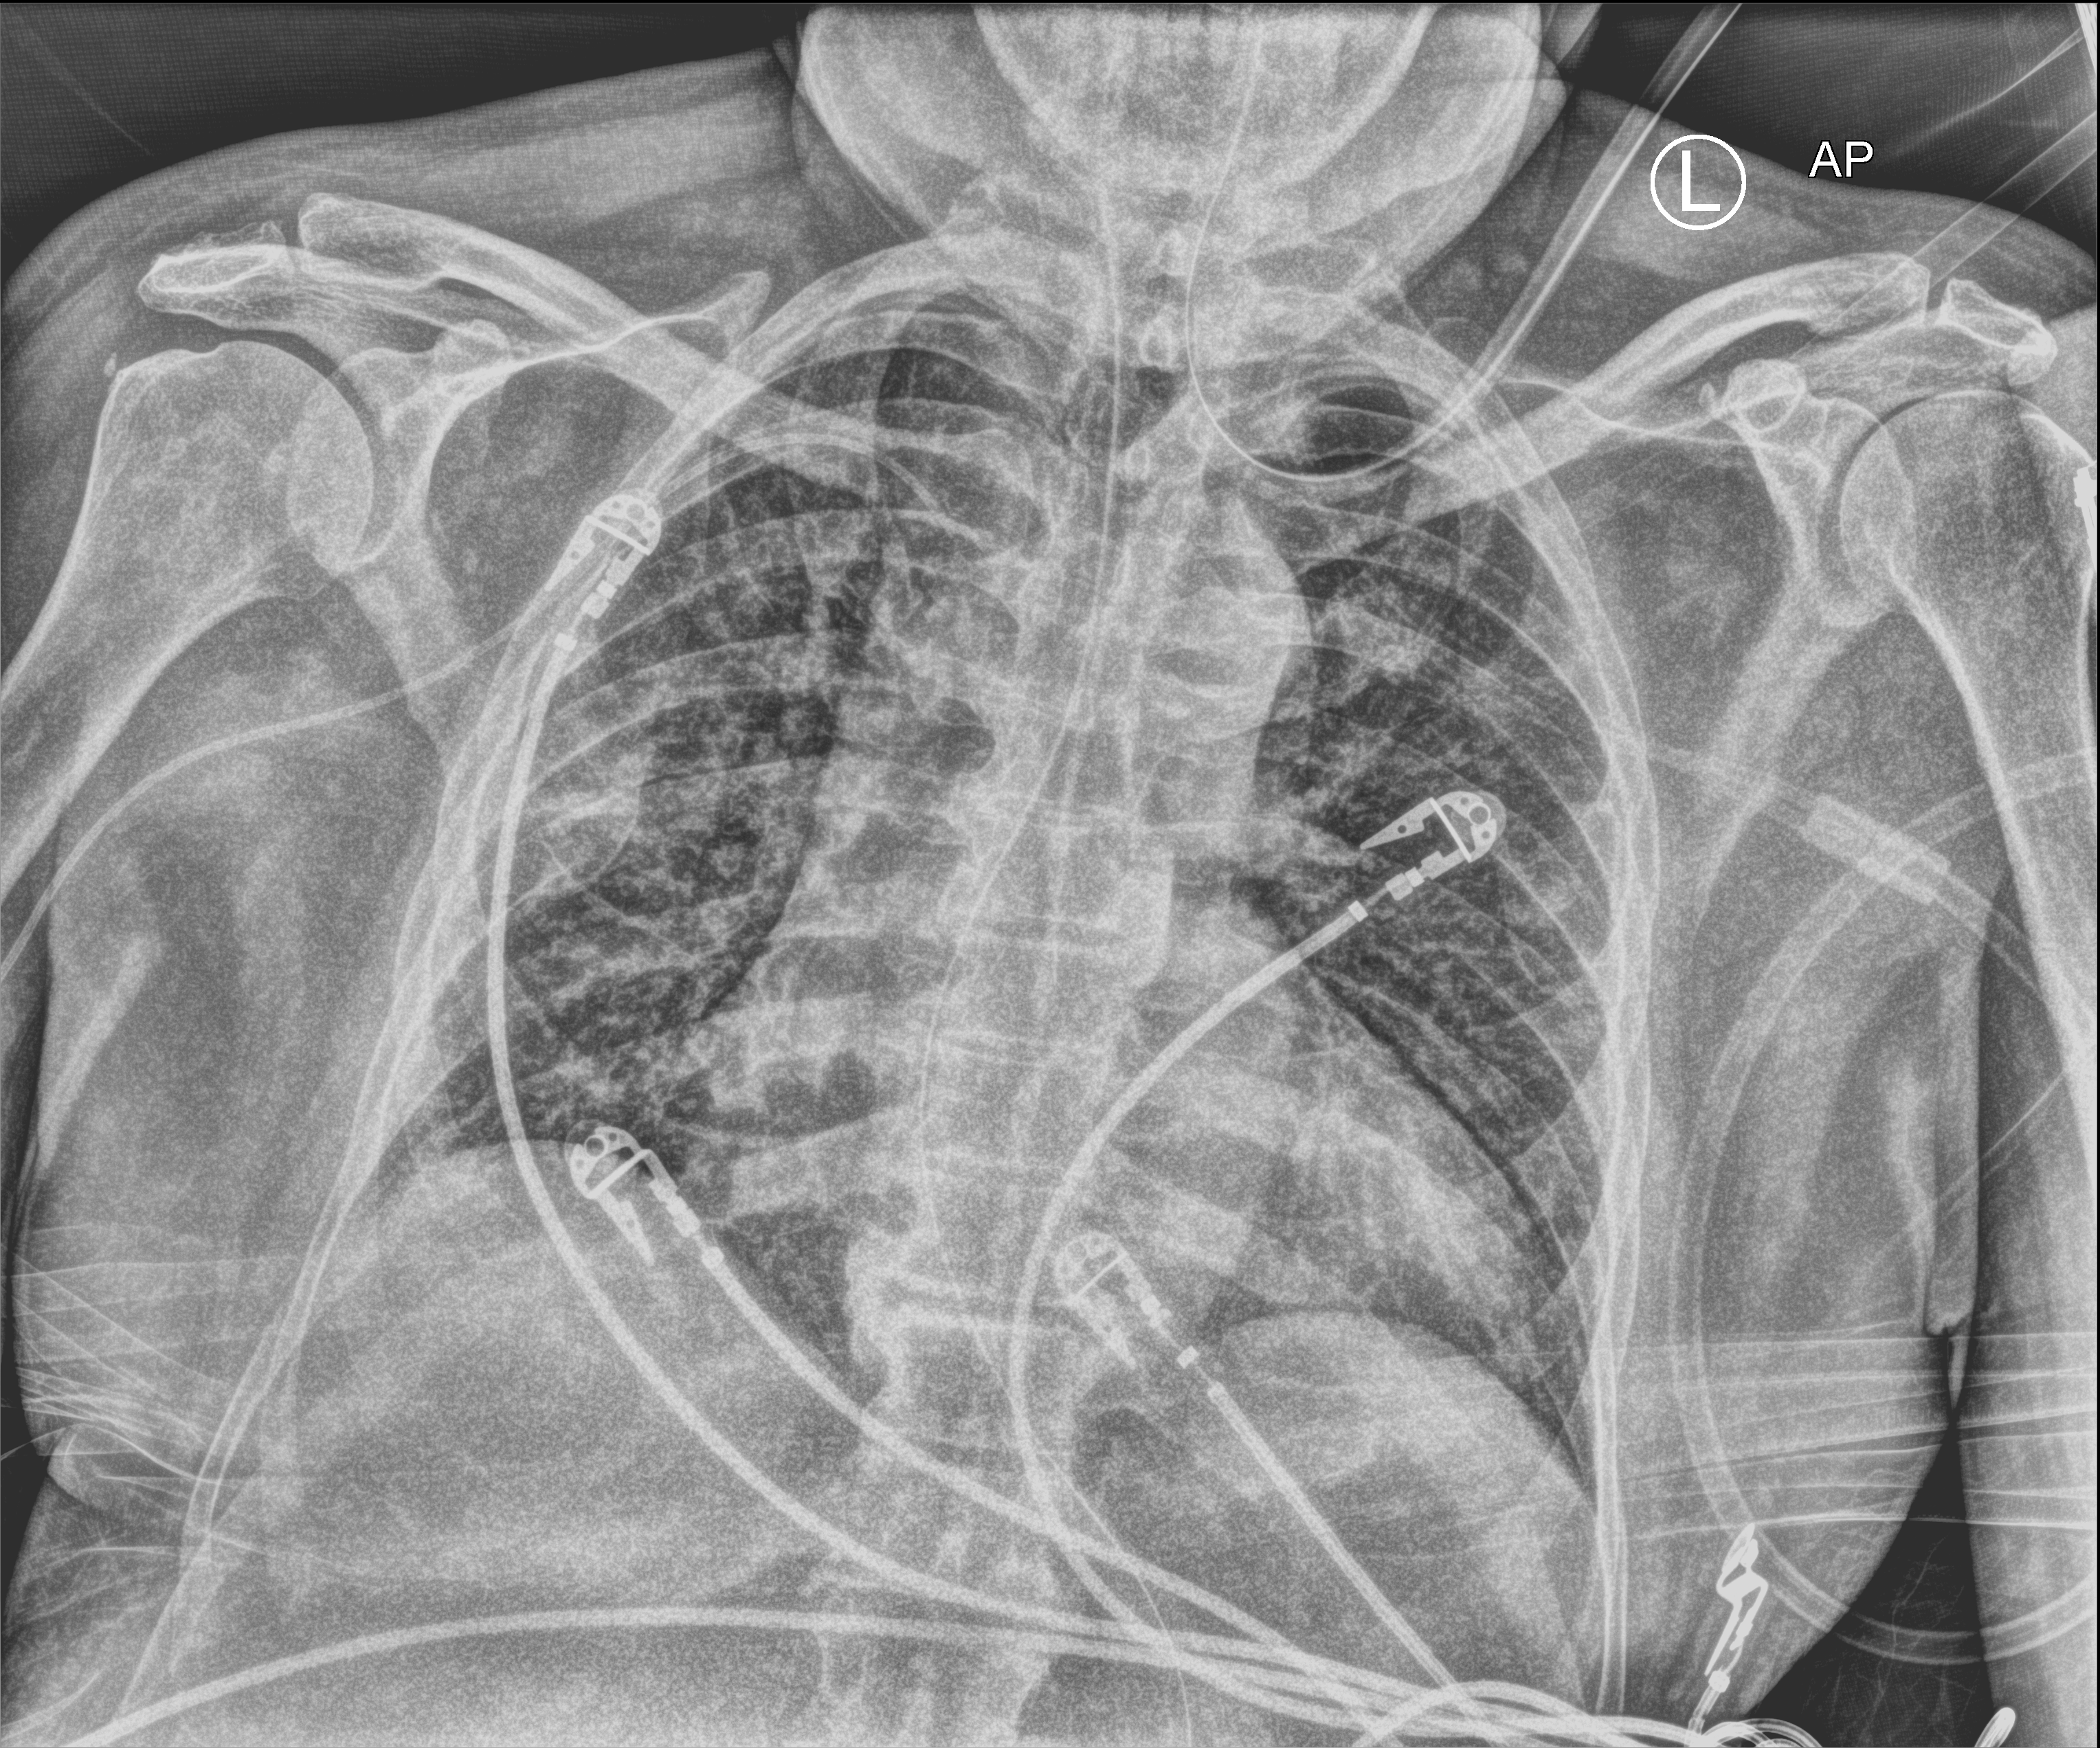
Chest X-ray (portable); anteroposterior (AP) projection. Male patient hospitalised with COVID-19, age 60–74 years.
Hospital-stay facts (about this admission, not read from this image; timing relative to this image not recorded): other chronic lung disease (admission record): yes; admitted to intensive care during this hospital stay: yes.